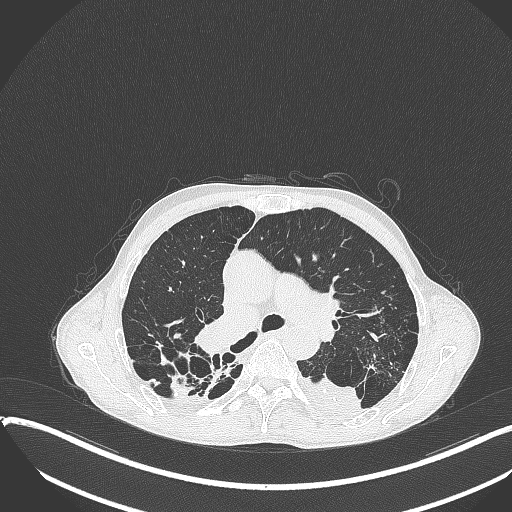
Chest CT, one axial slice. Slice 247 of 401 in the series (ordered by position). 120 kVp. Lung window (W 1500 / L -600 HU). 1 mm slice thickness. 512 × 512 image matrix, field of view 400 × 400 mm. Male patient, age 57 years. Case-level facts recorded for this patient, not image findings: clinical TNM (as recorded): T4 N0 M0.
Structures marked on this image (bounding box drawn by a radiologist):
- lung tumour (recorded histology: squamous cell carcinoma): bounding box <298,370,363,424> (left, top, right, bottom; pixels)